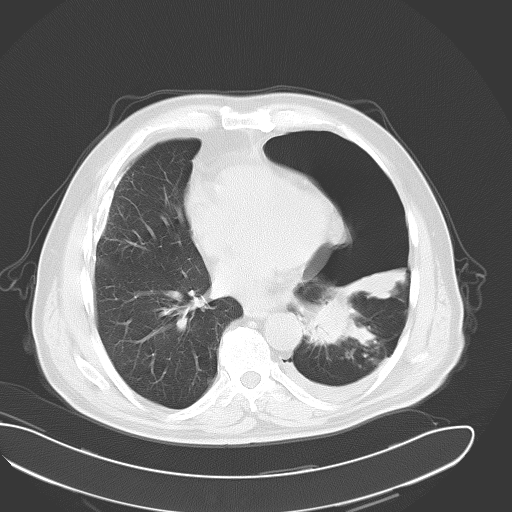
Chest CT, one axial slice. Slice 20 of 43 in the series (ordered by position). Reconstruction kernel B70f. Lung window (W 1500 / L -600 HU). 8 mm slice thickness. 512 × 512 image matrix, field of view 418 × 418 mm. Male patient, age 62 years. Case-level facts recorded for this patient, not image findings: clinical TNM (as recorded): T3 N0 M1.
Outlined on this slice (rectangle marked by the reading radiologist):
- lung tumour (recorded histology: adenocarcinoma): bounding box (x1, y1, x2, y2) in pixels: (297, 293, 376, 359)
- lung tumour (recorded histology: adenocarcinoma): (298, 291, 363, 349)